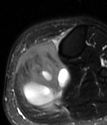
MRI of an extremity soft-tissue mass, one axial slice. Slice 30 of 78 in the series (ordered by position). T2-weighted fat-saturated. MR volume resampled by the dataset authors to the PET/CT grid (not the native acquisition matrix). 3.27 mm slice thickness. 107 × 125 image matrix, field of view 104 × 122 mm. Female patient. From the clinical record (not read from this slice): histological type: extraskeletal high grade osteogenic sarcoma; grade: high; site of the primary tumour: left calf.
Outlined on this slice (expert contour drawn on MRI and transferred to this co-registered scan by the dataset authors):
- gross tumour volume (mass): box from (x=17, y=43) to (x=68, y=108) px